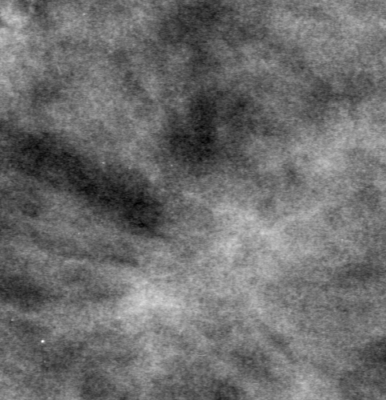
Region of interest cut from a scanned film mammogram (one marked finding); right breast; MLO view; BI-RADS breast density category 3 (scale 1–4).
- Finding: mass, shape architectural distortion, margins spiculated; BI-RADS assessment category 5; pathology (as recorded): malignant.